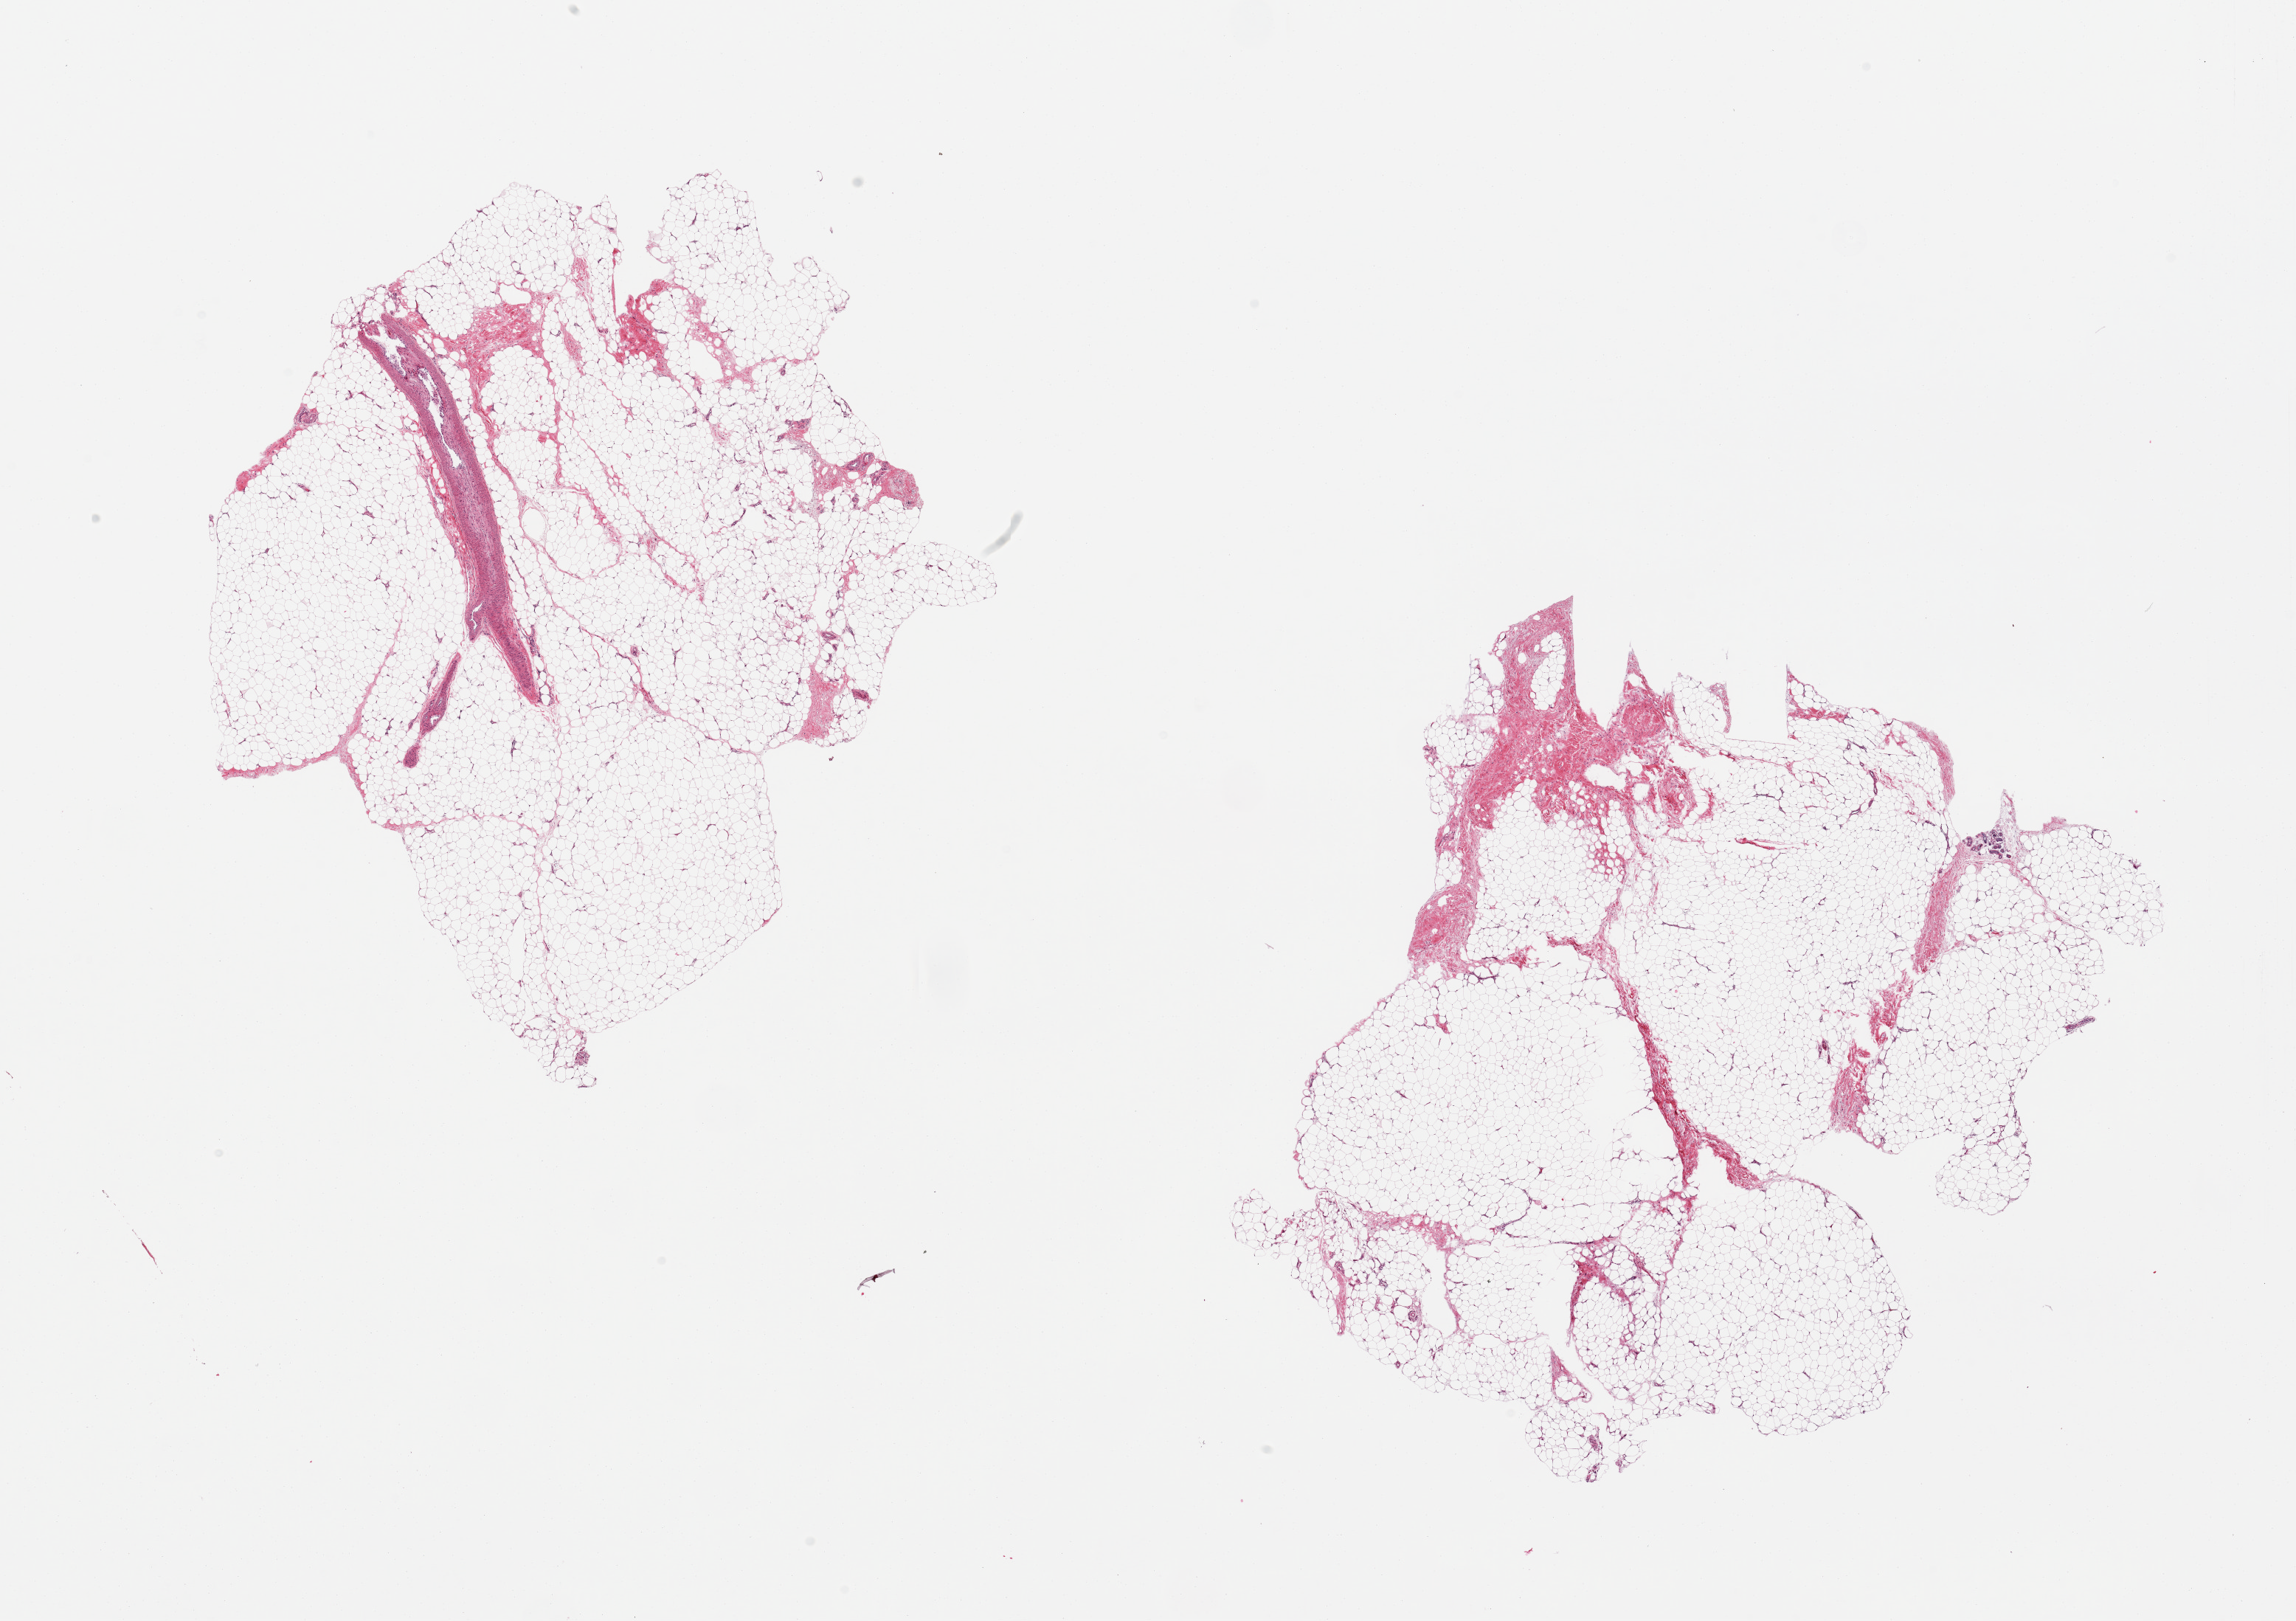
Whole-slide image, H&E stain, brightfield, whole scanned area (about 24.6 x 17.4 mm, acquisition: 20x scan) shown as a low-resolution overview. PAXgene-fixed, paraffin-embedded tissue. Target tissue: adipose tissue. Tissue donor sample. Female donor.
Review note (as recorded): 2 pieces; 5% fibrous content.